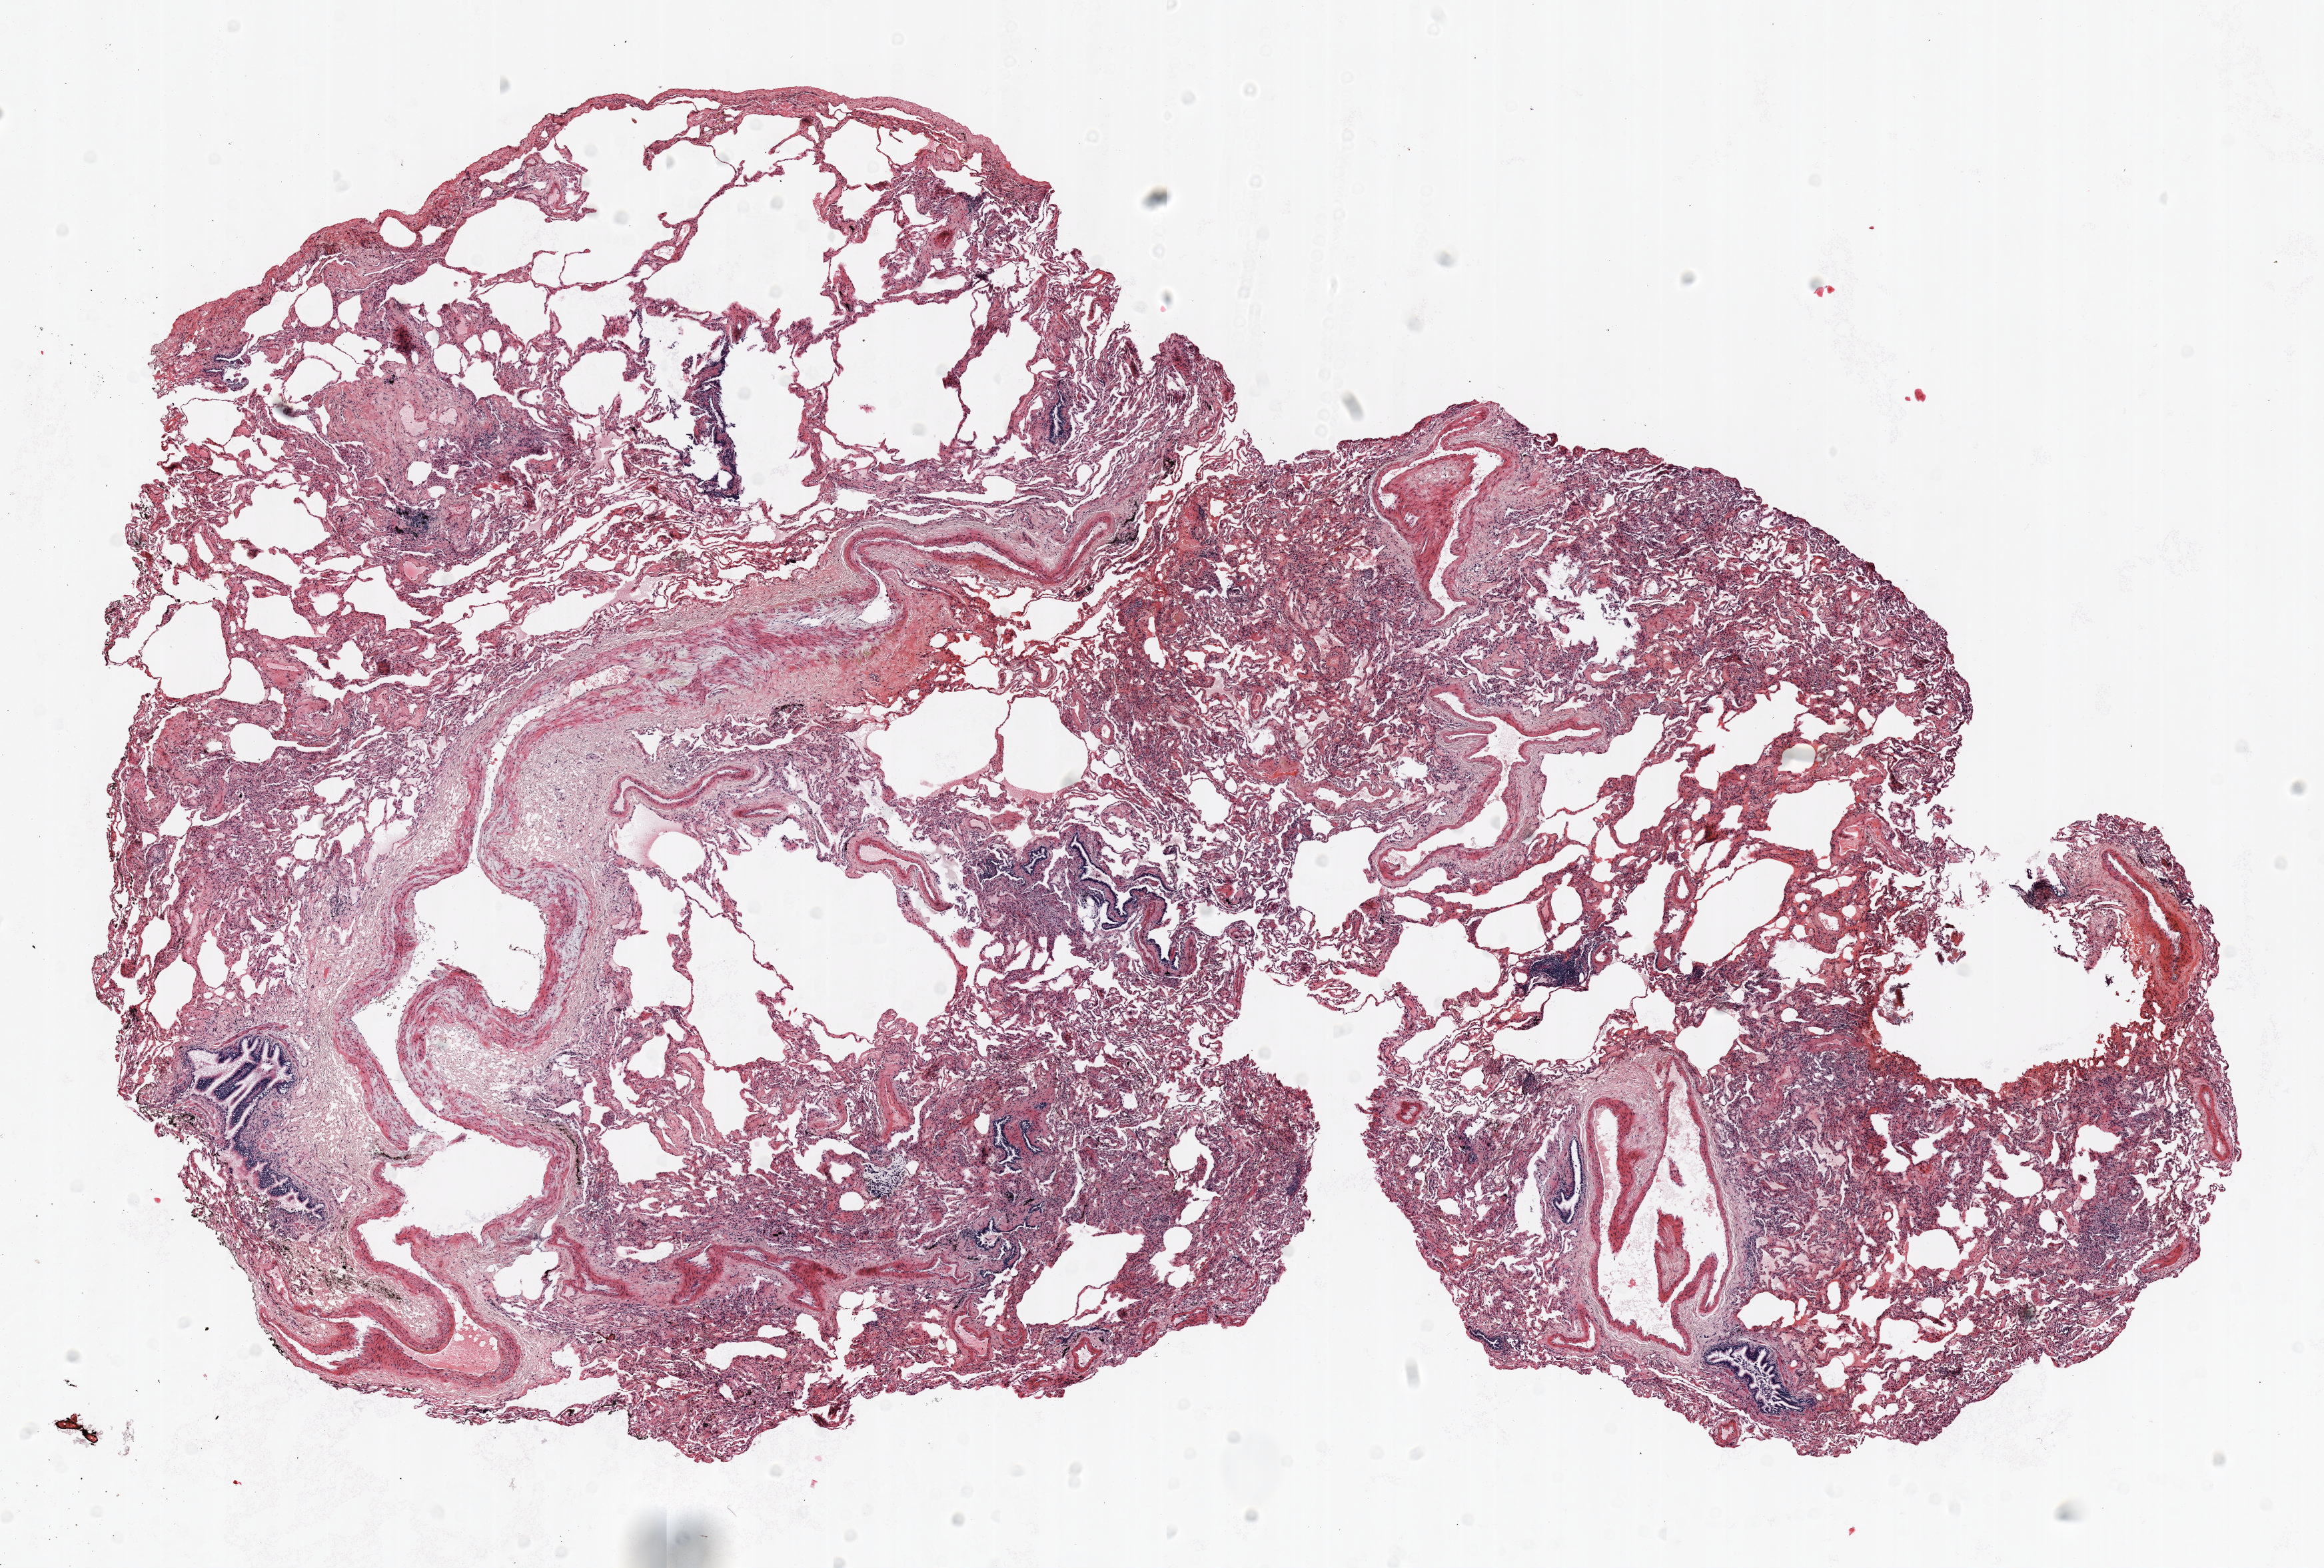
H&E whole-slide image, whole scanned area (about 14.0 x 9.5 mm) shown as a low-resolution overview. Formalin-fixed paraffin-embedded (FFPE) section. Lung. Female patient, aged 64 at enrolment. Former smoker at enrolment. Grade: well differentiated (G1).
Participant's lung-cancer diagnosis: Bronchiolo-alveolar adenocarcinoma, NOS (ICD-O-3 8250/3). ICD-O-3 topography: lower lobe of lung (C34.3). Stage (AJCC 6th edition): IA. Tumour size (pathology): 8 mm. Primary tumour location (clinical record): left lower lobe.